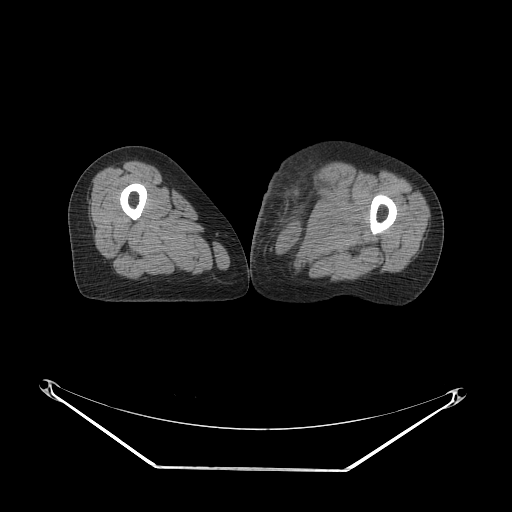
CT of an extremity soft-tissue mass (from a PET/CT study), one axial slice. Slice 46 of 91 in the series (ordered by position). Soft-tissue window (W 400 / L 40 HU). 512 × 512 image matrix, field of view 500 × 500 mm. Female patient. From the clinical record (not read from this slice): histological type: pleomorphic leiomyosarcoma; grade: high; site of the primary tumour: left thigh.
Structures marked on this image (expert contour drawn on MRI and transferred to this co-registered scan by the dataset authors):
- gross tumour volume including surrounding oedema: bounding box (x1, y1, x2, y2) in pixels: (263, 167, 337, 238)